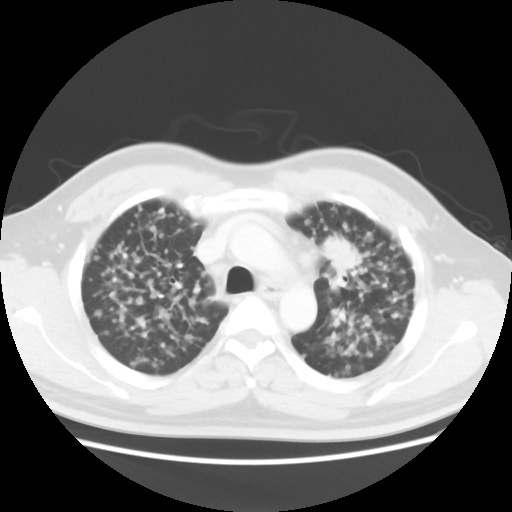
Chest CT, one axial slice. 120 kVp. Lung window (W 1500 / L -600 HU). 512 × 512 image matrix, field of view 366 × 366 mm. Patient: male, 41 years. From the clinical record (not read from this slice): clinical TNM (as recorded): T1c N3 M1b.
Annotated regions visible in this slice (rectangle marked by the reading radiologist):
- lung tumour (recorded histology: adenocarcinoma): bounding box <316,231,368,291> (left, top, right, bottom; pixels)